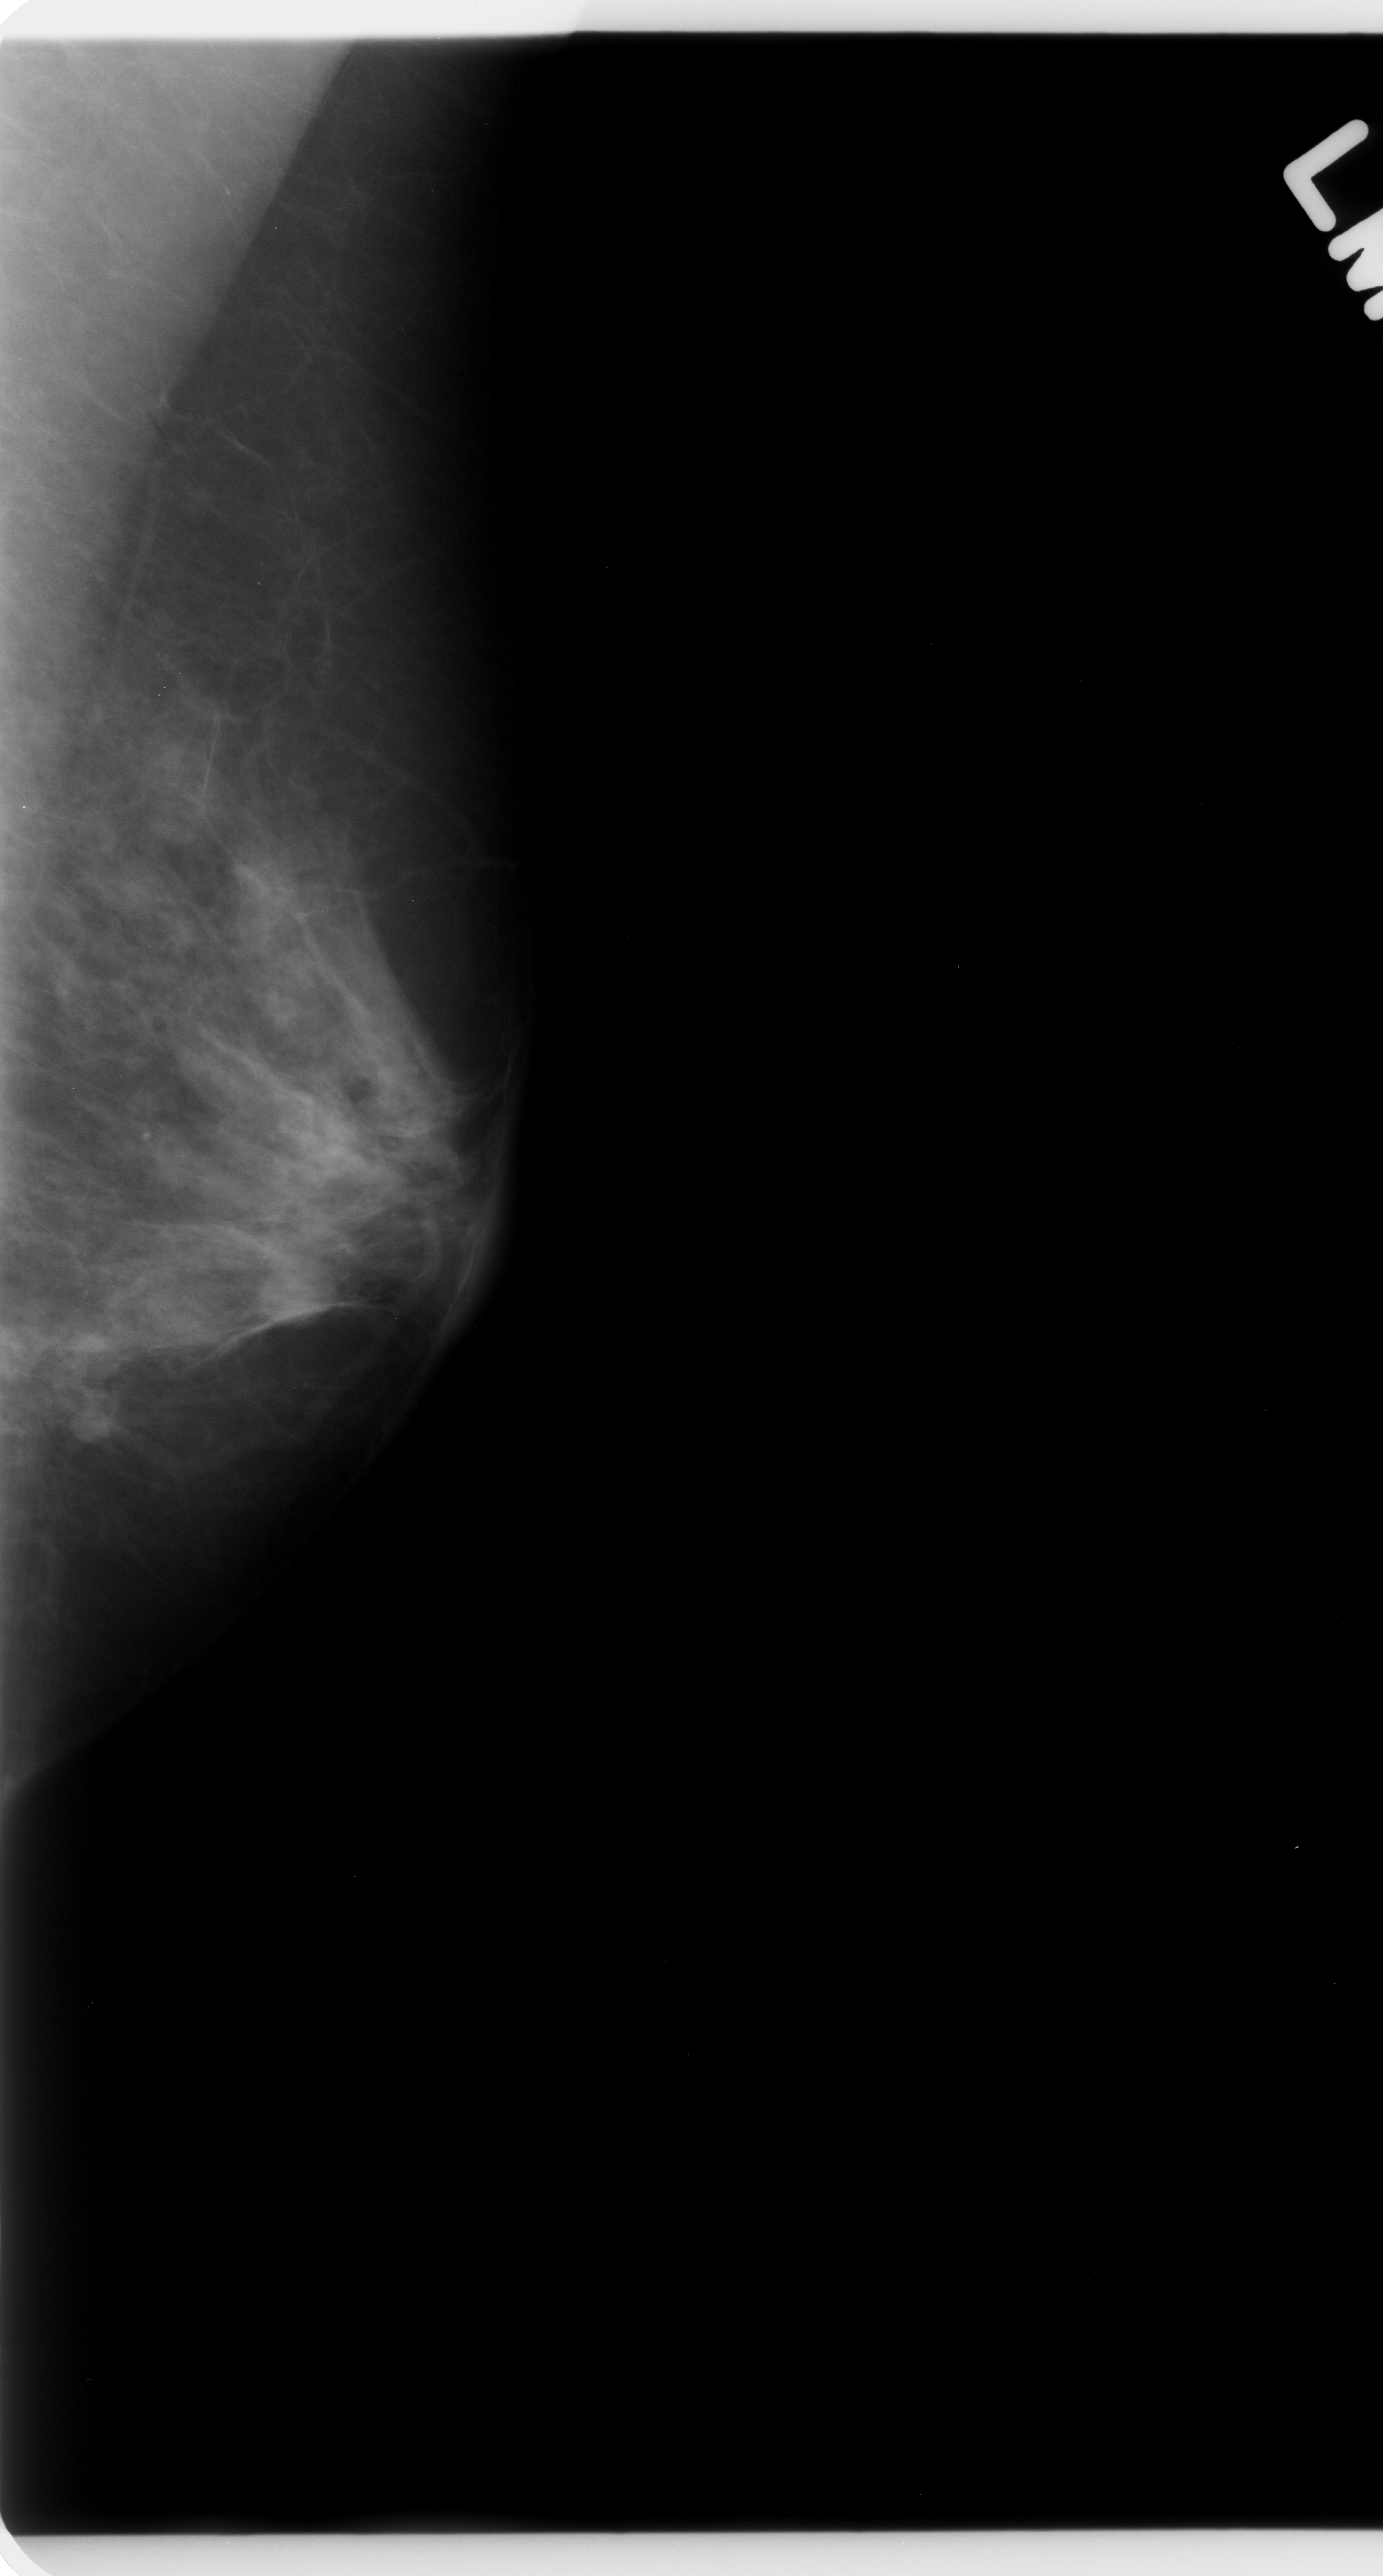
Mammogram (digitized film); left breast; MLO view; breast composition: heterogeneously dense (BI-RADS density category 3 of 4); 1383 × 2576 image matrix.
Expert-marked regions of interest on this image (one box per marked abnormality):
- mass, shape oval, margins circumscribed; BI-RADS assessment category 4; pathology (as recorded): benign: bounding box (x1, y1, x2, y2) in pixels: (224, 1211, 352, 1336)